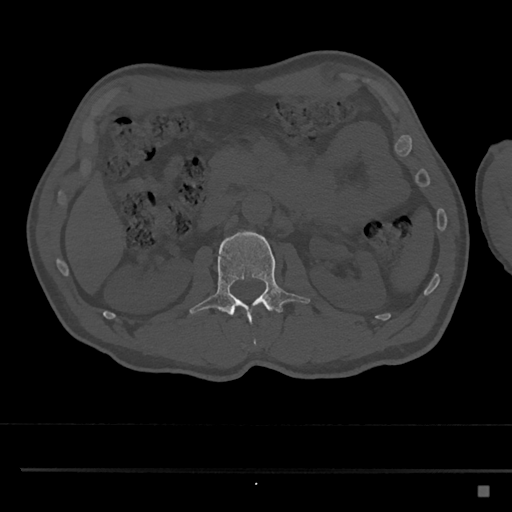
CT including the spine, one axial slice. Slice 768 of 797 in the series (ordered by position). Reconstruction kernel Br40s/3. 120 kVp. Bone window (W 1800 / L 400 HU). 512 × 512 image matrix. Patient: male, 59 years. From the clinical record (not read from this slice): primary cancer: prostate.
Outlined on this slice (semi-automatic segmentation, software-assisted and operator-edited):
- L2 vertebra: bounding box <190,230,310,348> (left, top, right, bottom; pixels)